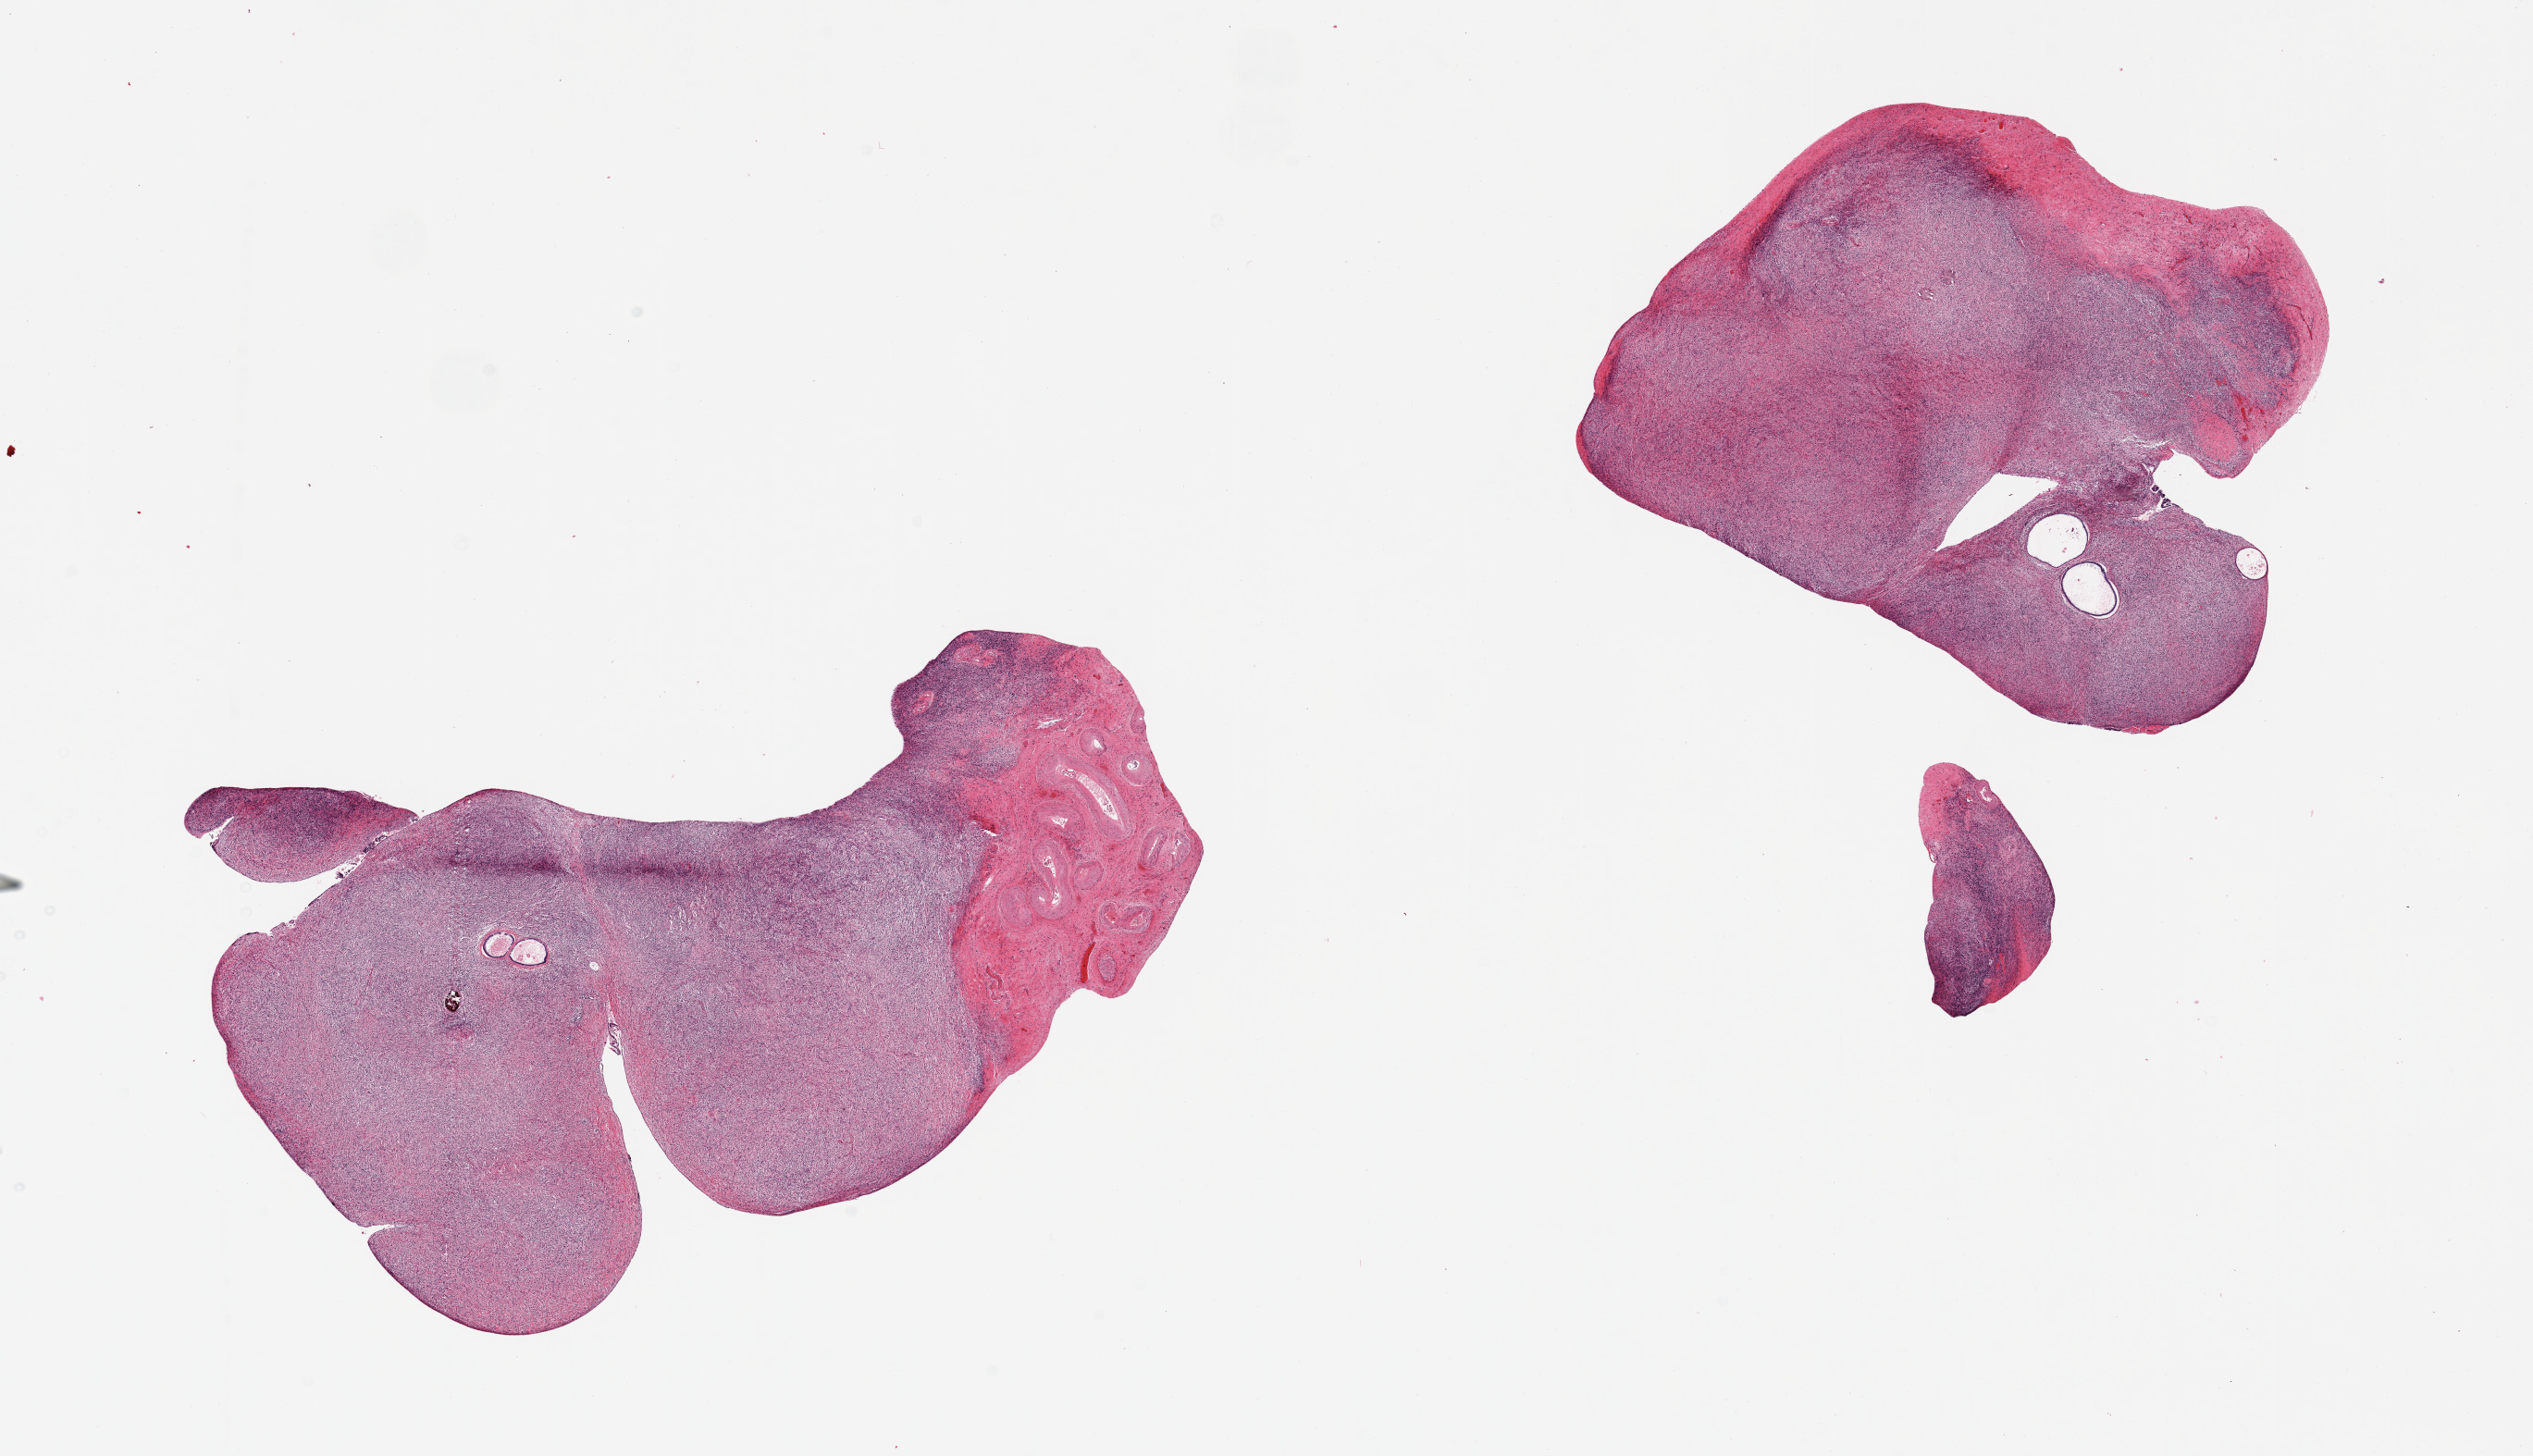
Whole-slide image, H&E stain, brightfield — a low-resolution overview of the entire scanned area, about 21.7 x 12.5 mm (slide scanned at 20x). PAXgene-fixed, paraffin-embedded tissue. Sampled site (target tissue): ovary. Donor tissue sample. Donor sex: female.
* pathologist's review note for this sample: 2 pieces; atrophic follicles